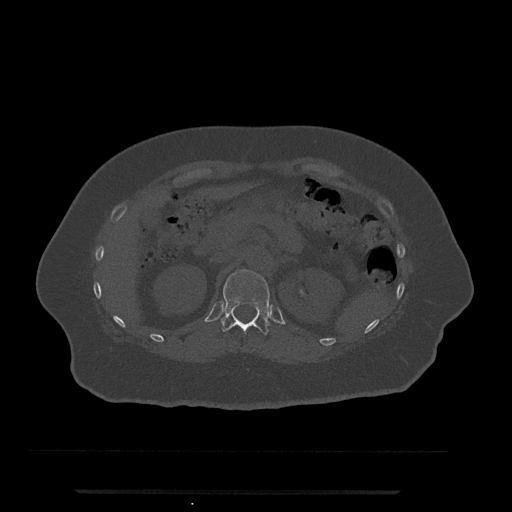
CT including the spine, one axial slice. Position 170 of 797 along the scan axis. 120 kVp. Bone window (W 1800 / L 400 HU). 0.5 mm slice thickness. 512 × 512 image matrix, field of view 440 × 440 mm. Patient: female, 51 years. Case-level facts recorded for this patient, not image findings: primary cancer: neuro; vertebrae with lytic lesions (as recorded): T8.
Annotated regions visible in this slice (semi-automatic segmentation, software-assisted and operator-edited):
- T12 vertebra: bounding box <221,270,270,335> (left, top, right, bottom; pixels)